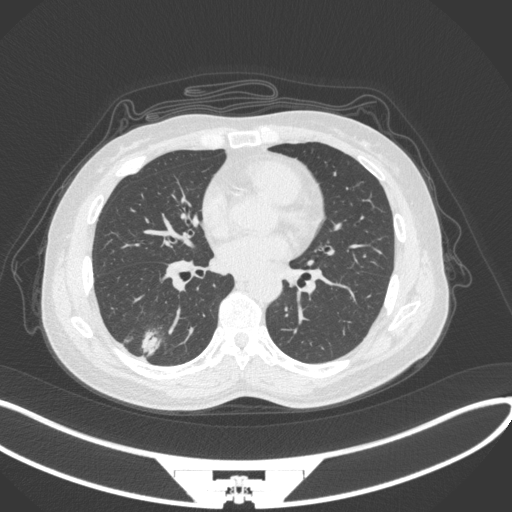
Chest CT, one axial slice. Reconstruction kernel B31f. Lung window (W 1500 / L -600 HU). 512 × 512 image matrix, field of view 400 × 400 mm. Patient: female, 55 years. From the clinical record (not read from this slice): clinical TNM (as recorded): T1c N1 M0.
Annotated regions visible in this slice (rectangle marked by the reading radiologist):
- lung tumour (recorded histology: adenocarcinoma): bounding box [x1, y1, x2, y2] px = [134, 323, 165, 358]